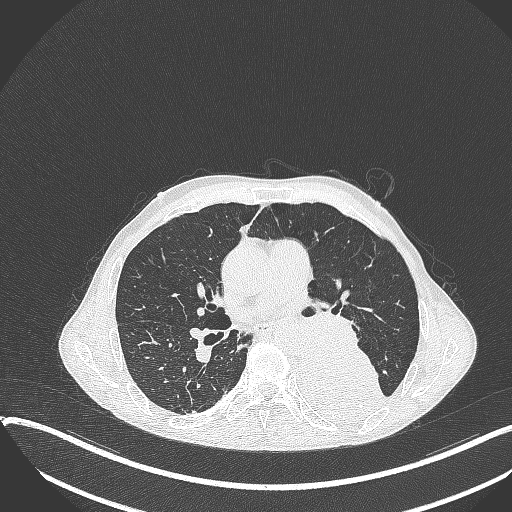
Chest CT, one axial slice. Slice 202 of 401 in the series (ordered by position). Lung window (W 1500 / L -600 HU). 1 mm slice thickness. 512 × 512 image matrix, field of view 400 × 400 mm. Male patient, age 57 years. Case-level facts recorded for this patient, not image findings: clinical TNM (as recorded): T4 N0 M0.
Structures marked on this image (bounding box drawn by a radiologist):
- lung tumour (recorded histology: squamous cell carcinoma): bounding box (x1, y1, x2, y2) in pixels: (290, 341, 386, 426)